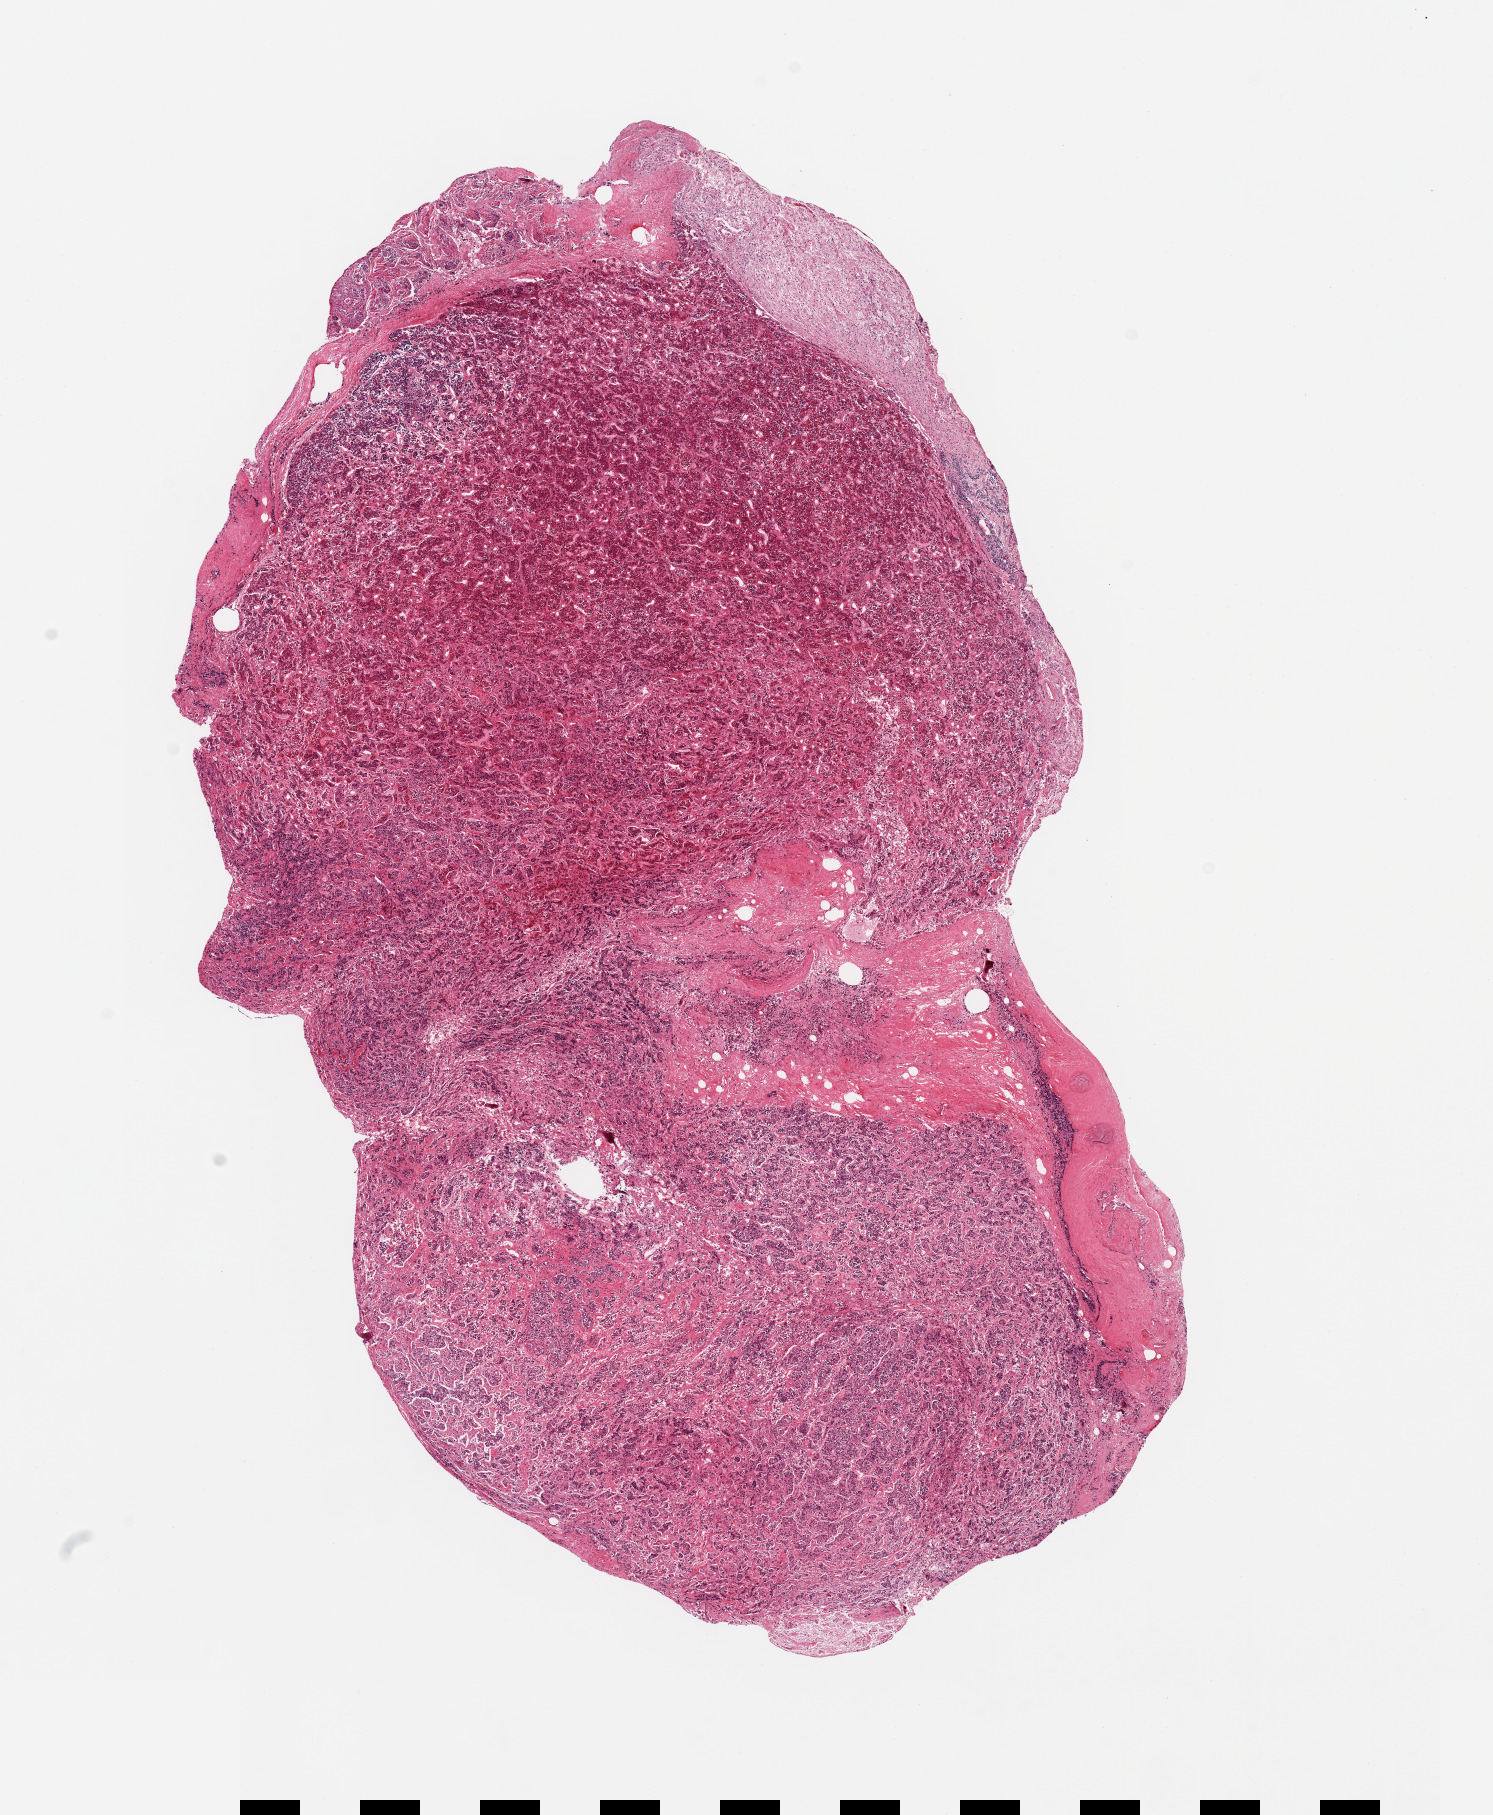
Whole-slide image, H&E stain — whole scanned area (about 11.8 x 14.4 mm) shown as a low-resolution overview, PAXgene-fixed paraffin-embedded (PFPE) section, section of pituitary (target tissue), donor tissue sample.
• review note (as recorded): 1 piece, mainly adenohypophysis, 4x1mm nubbin of neurohypophysis